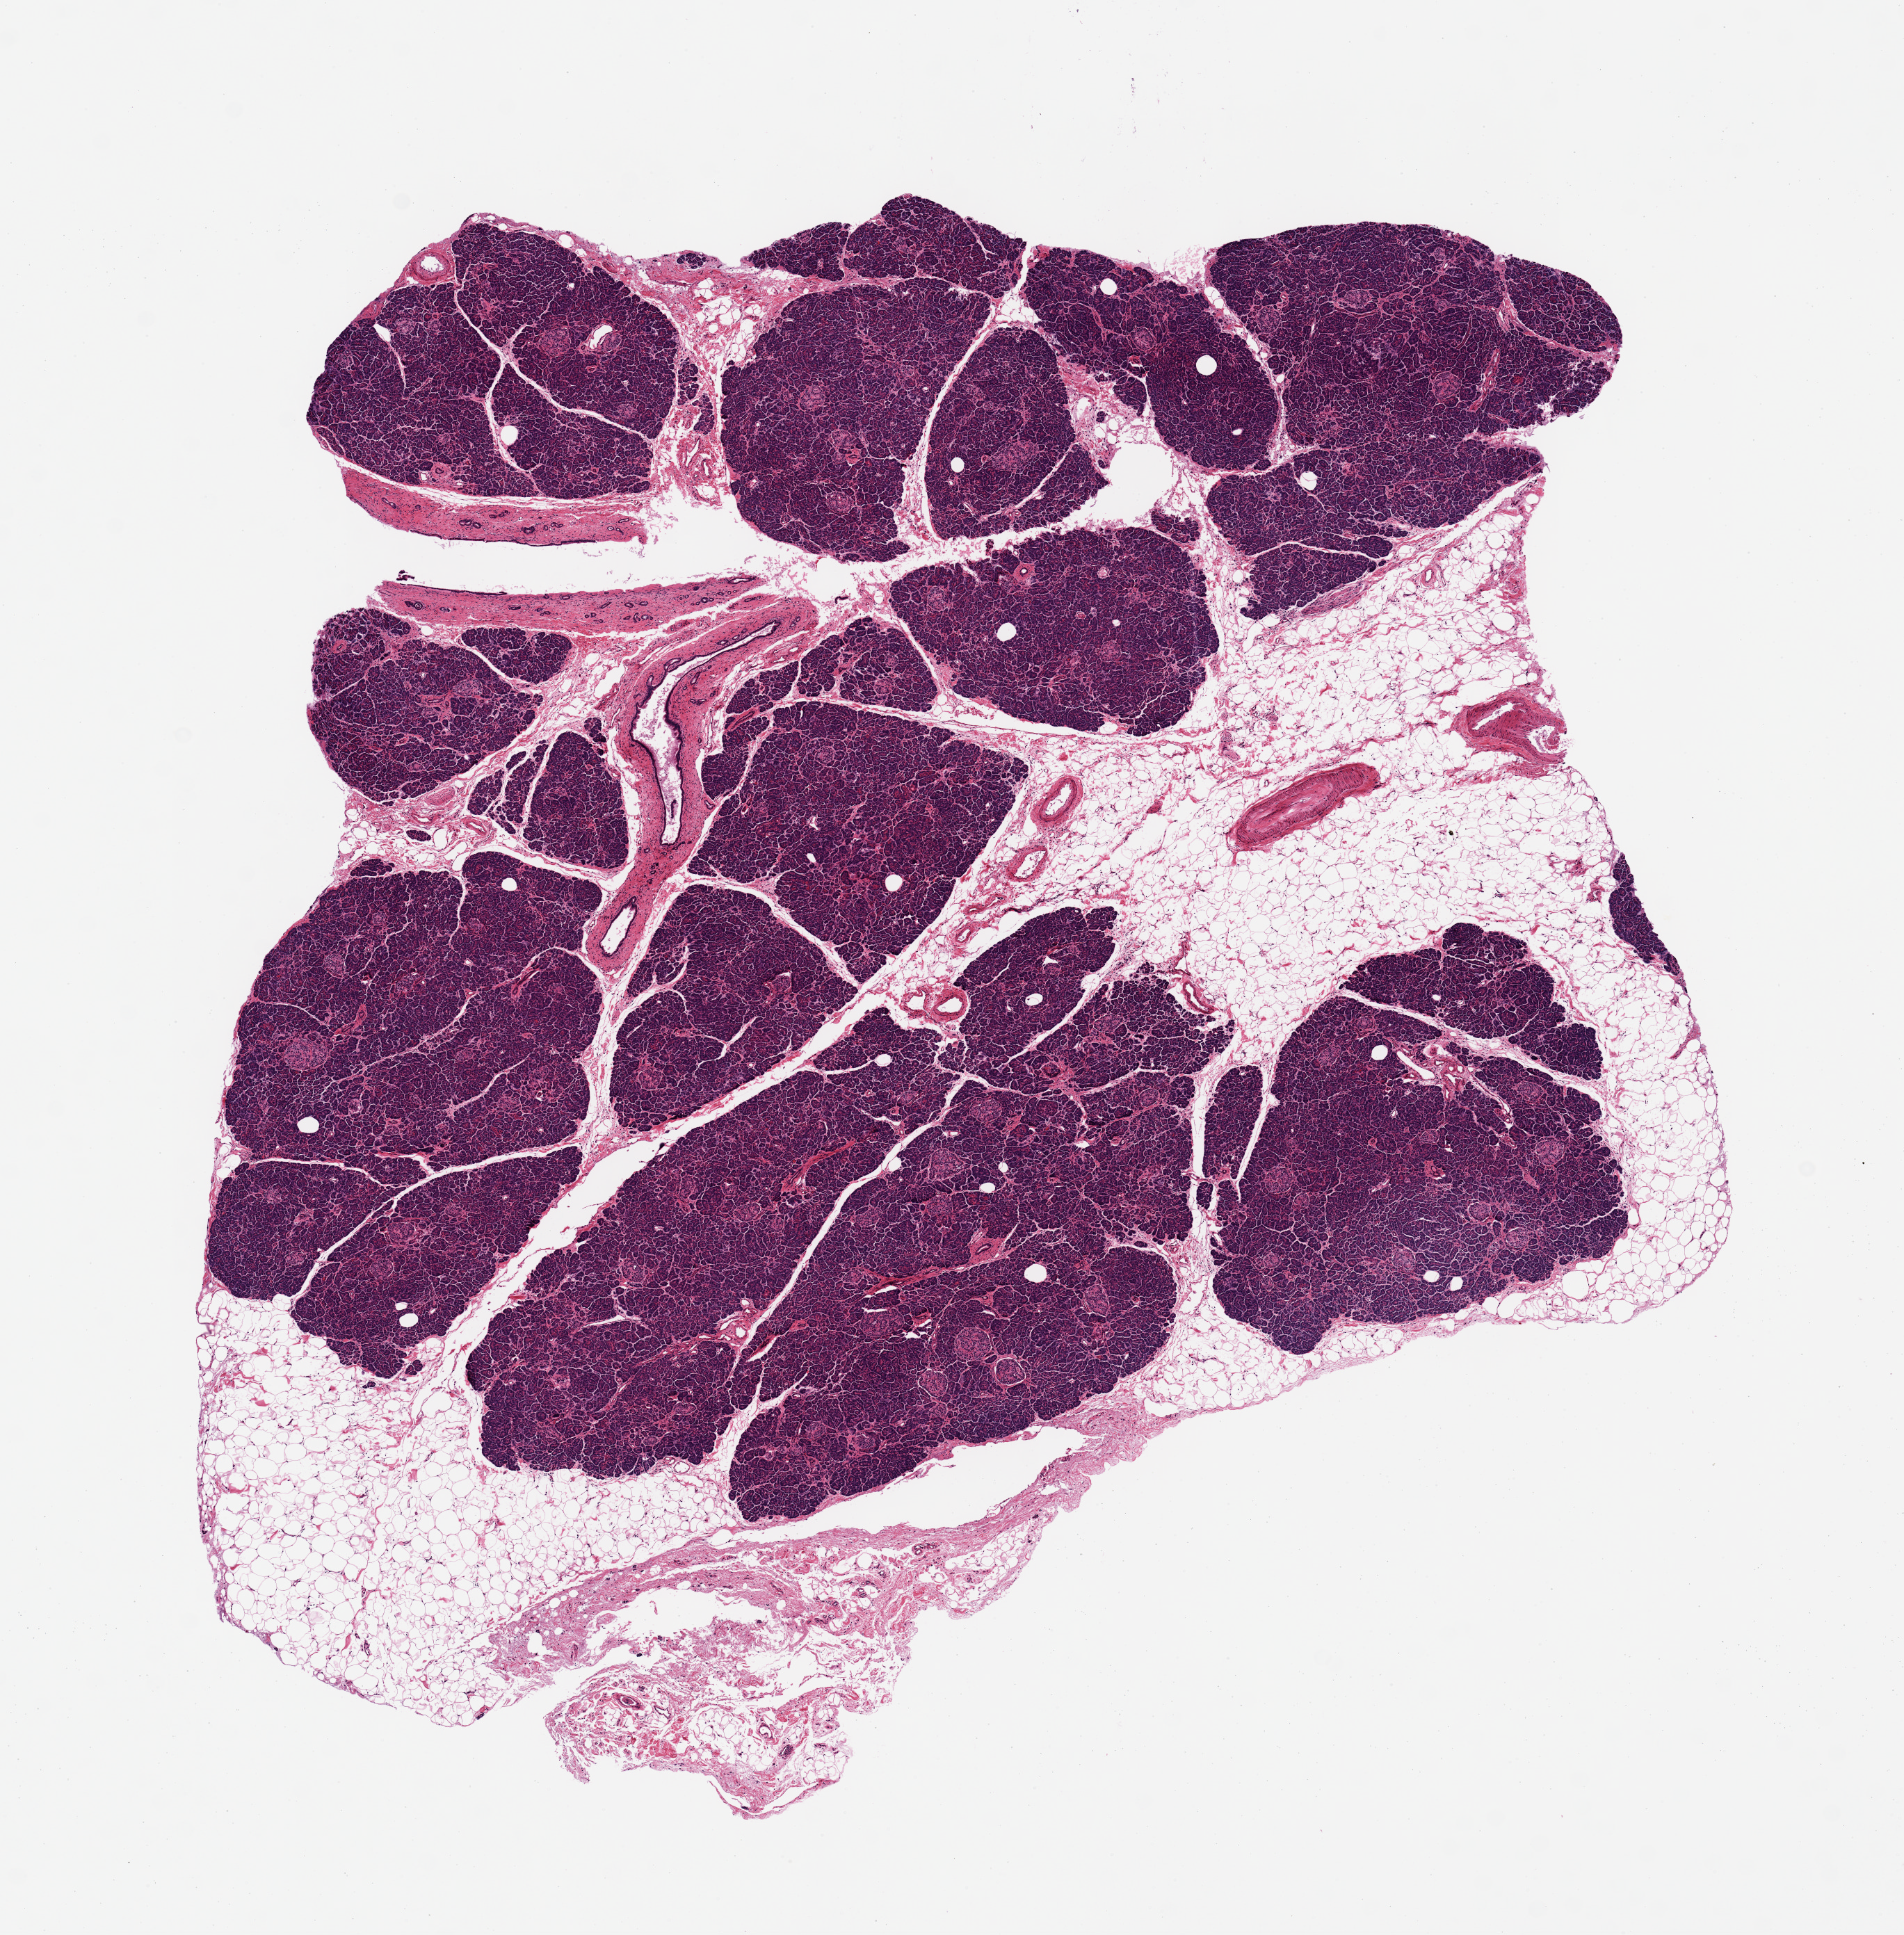
Digitized hematoxylin and eosin (H&E)-stained section — whole scanned area (about 10.8 x 11.0 mm) shown as a low-resolution overview. PAXgene-fixed paraffin-embedded (PFPE) section. Target tissue: pancreas. Tissue donor sample. Female donor.
• pathologist's review note for this sample: Fat is about 20% of aliquot